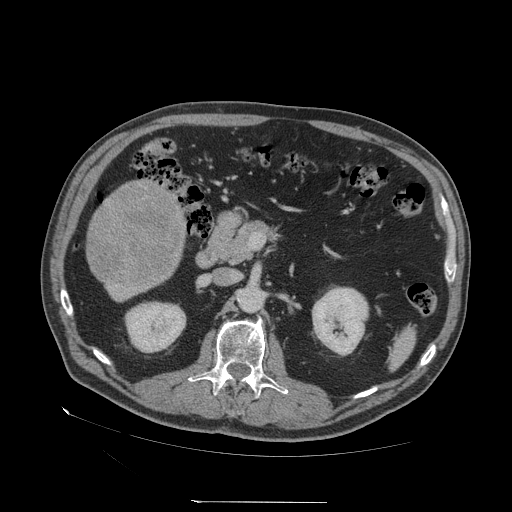
Contrast-enhanced abdominal CT (liver protocol), one axial slice; position 12 of 83 along the scan axis; reconstruction kernel STANDARD; soft-tissue window (W 400 / L 40 HU); 2.5 mm slice thickness; 512 × 512 image matrix, field of view 460 × 460 mm. From the clinical record (not read from this slice): diagnosis: hepatocellular carcinoma (patient treated with transarterial chemoembolisation; whether this scan precedes or follows treatment is not stated here); TNM stage (as recorded): Stage-I; Child-Pugh class: A; tumour nodularity: uninodular.
Outlined on this slice (semi-automatic segmentation, software-assisted and operator-edited):
- liver parenchyma outside the tumour (the mass and vessels are separate outlines, so this box may not span the whole liver): bounding box [x1, y1, x2, y2] px = [106, 196, 184, 300]
- mass: [90, 185, 184, 283]